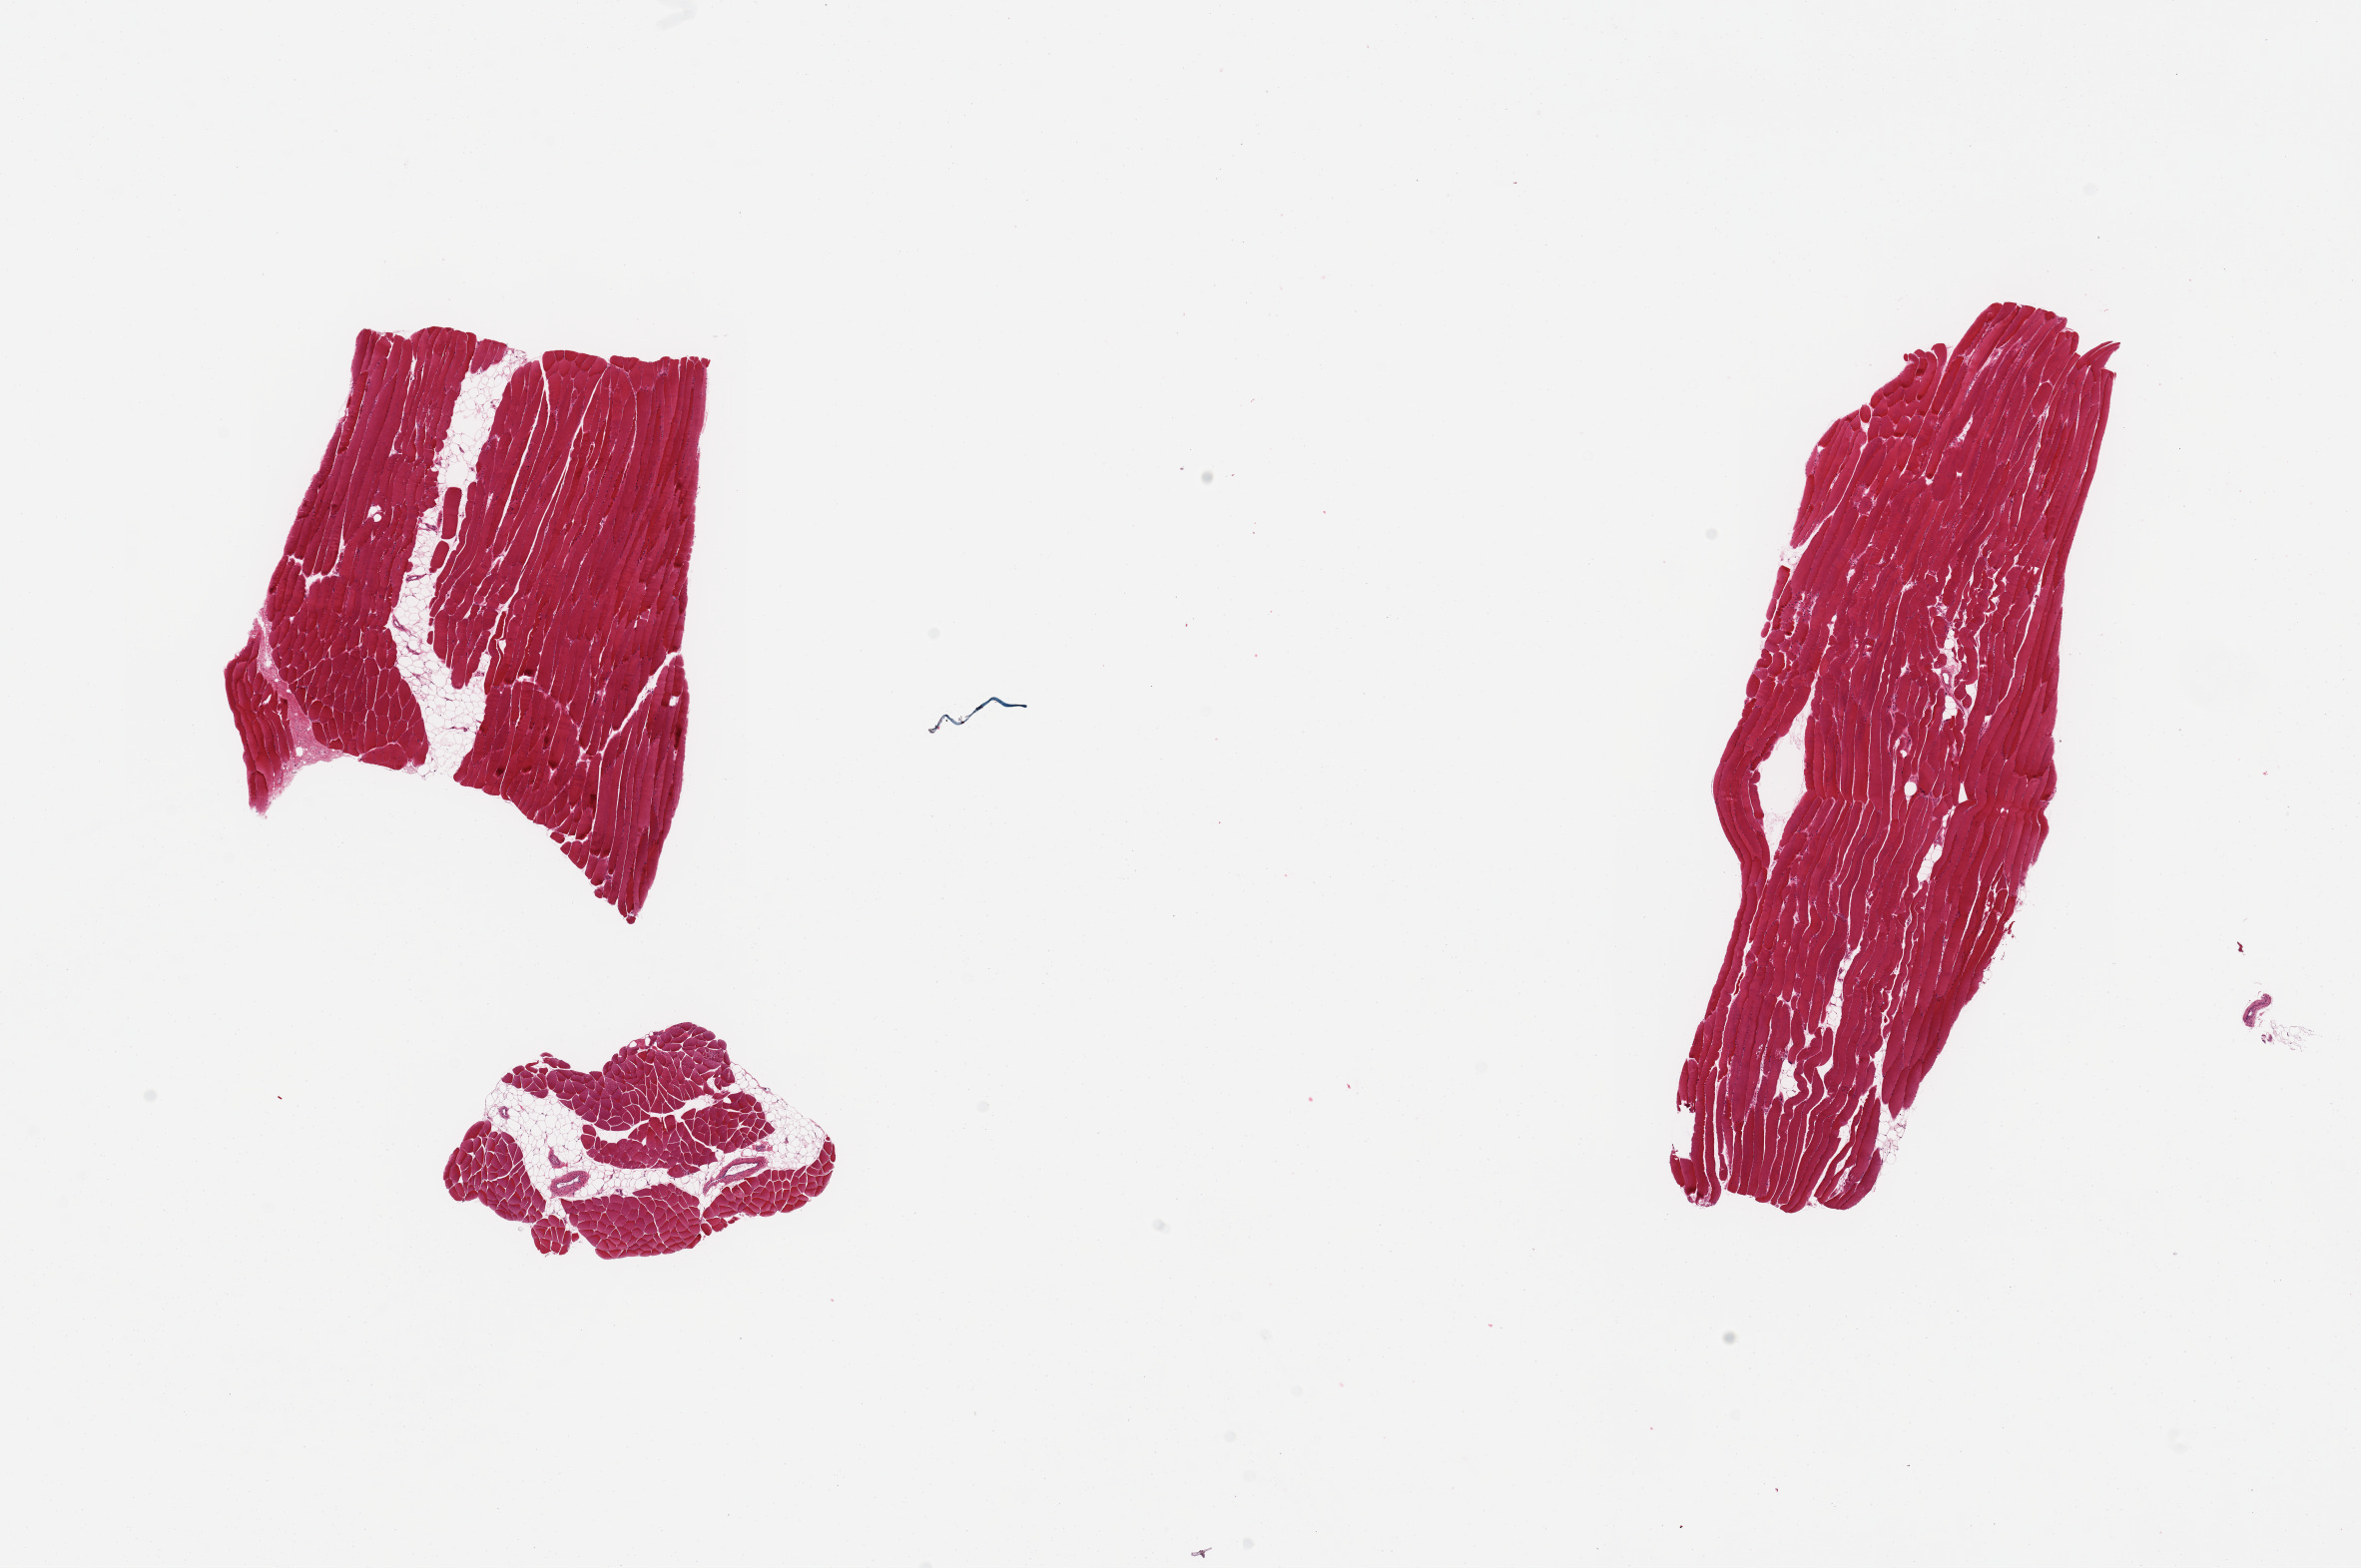
H&E whole-slide image — whole scanned area (about 18.7 x 12.4 mm, from a 20x scan) shown as a low-resolution overview; PAXgene-fixed paraffin-embedded (PFPE) section; sampled site (target tissue): skeletal muscle; tissue donor sample. Male donor.
Pathologist's review note for this sample: 3 pieces; 5-10% internal fat.